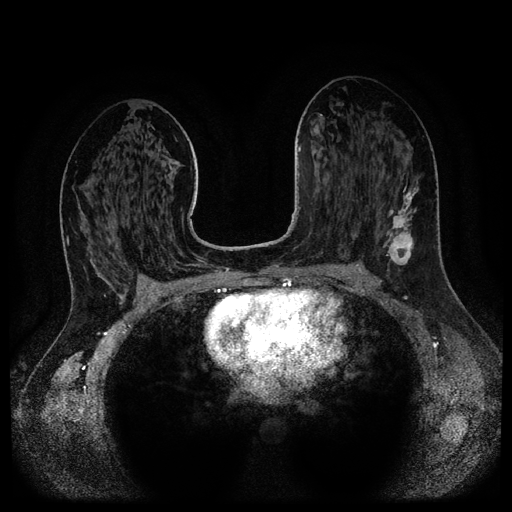
Breast MRI (dynamic contrast-enhanced, multi-phase), one axial slice; position 61 of 116 along the scan axis; dynamic contrast-enhanced series, time point 2 of 5 at this slice position (early post-contrast); 1.5 T; TE 2.6 ms, TR 5.3 ms; 2.1 mm slice thickness; 512 × 512 image matrix, field of view 360 × 360 mm. Patient: female, 37 years.
Outlined on this slice (semi-automatic segmentation, software-assisted and operator-edited):
- breast lesion (labelled 'tumour' in the annotation; benign lesions carry a separate 'benign' label): bounding box (x1, y1, x2, y2) in pixels: (383, 184, 419, 271)